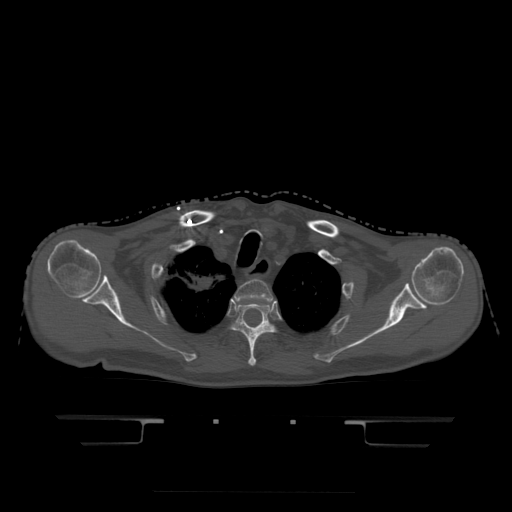
CT including the spine, one axial slice. Slice 374 of 522 in the series (ordered by position). Bone window (W 1800 / L 400 HU). 1.25 mm slice thickness. 512 × 512 image matrix, field of view 436 × 436 mm. Patient age 68 years. Case-level facts recorded for this patient, not image findings: primary cancer: urothelial.
Structures marked on this image (semi-automatically segmented with operator editing):
- T2 vertebra: bounding box <234,280,273,301> (left, top, right, bottom; pixels)
- T3 vertebra: <233,300,274,367>